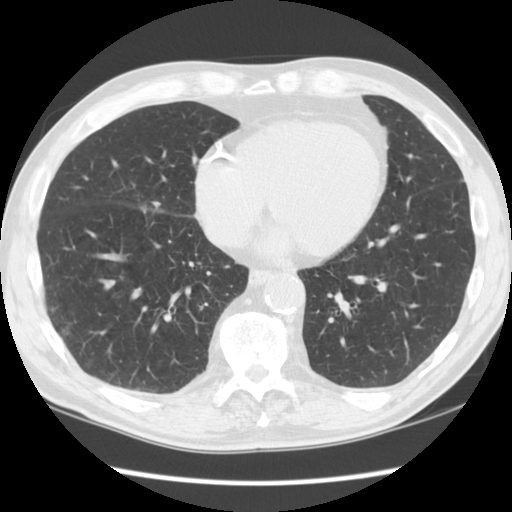
Low-dose screening chest CT, axial slice, second annual screen, lung window (W 1500 / L -600 HU), standard (soft-tissue) reconstruction kernel (STANDARD), slice 87 of 132 in the series. Male, age 64 years at enrolment.
- Expert reader's lesion annotation, bounding box (x1, y1, x2, y2) in pixels: (126, 191, 174, 223).
- The exam's reader record, not a measurement of the box and not confirmed to be the same lesion: non-calcified nodule or mass ≥4 mm, right middle lobe, 6 × 5 mm, smooth margins, soft tissue attenuation, pre-existing on the prior screen: no.
- Official screen result: positive, other.
- Later outcome: lung cancer diagnosed 300 days after this screen (after the third annual screen) — non-small cell carcinoma, right middle lobe, poorly differentiated (G3), stage IIIA (AJCC 6th edition), 20 mm at pathology.